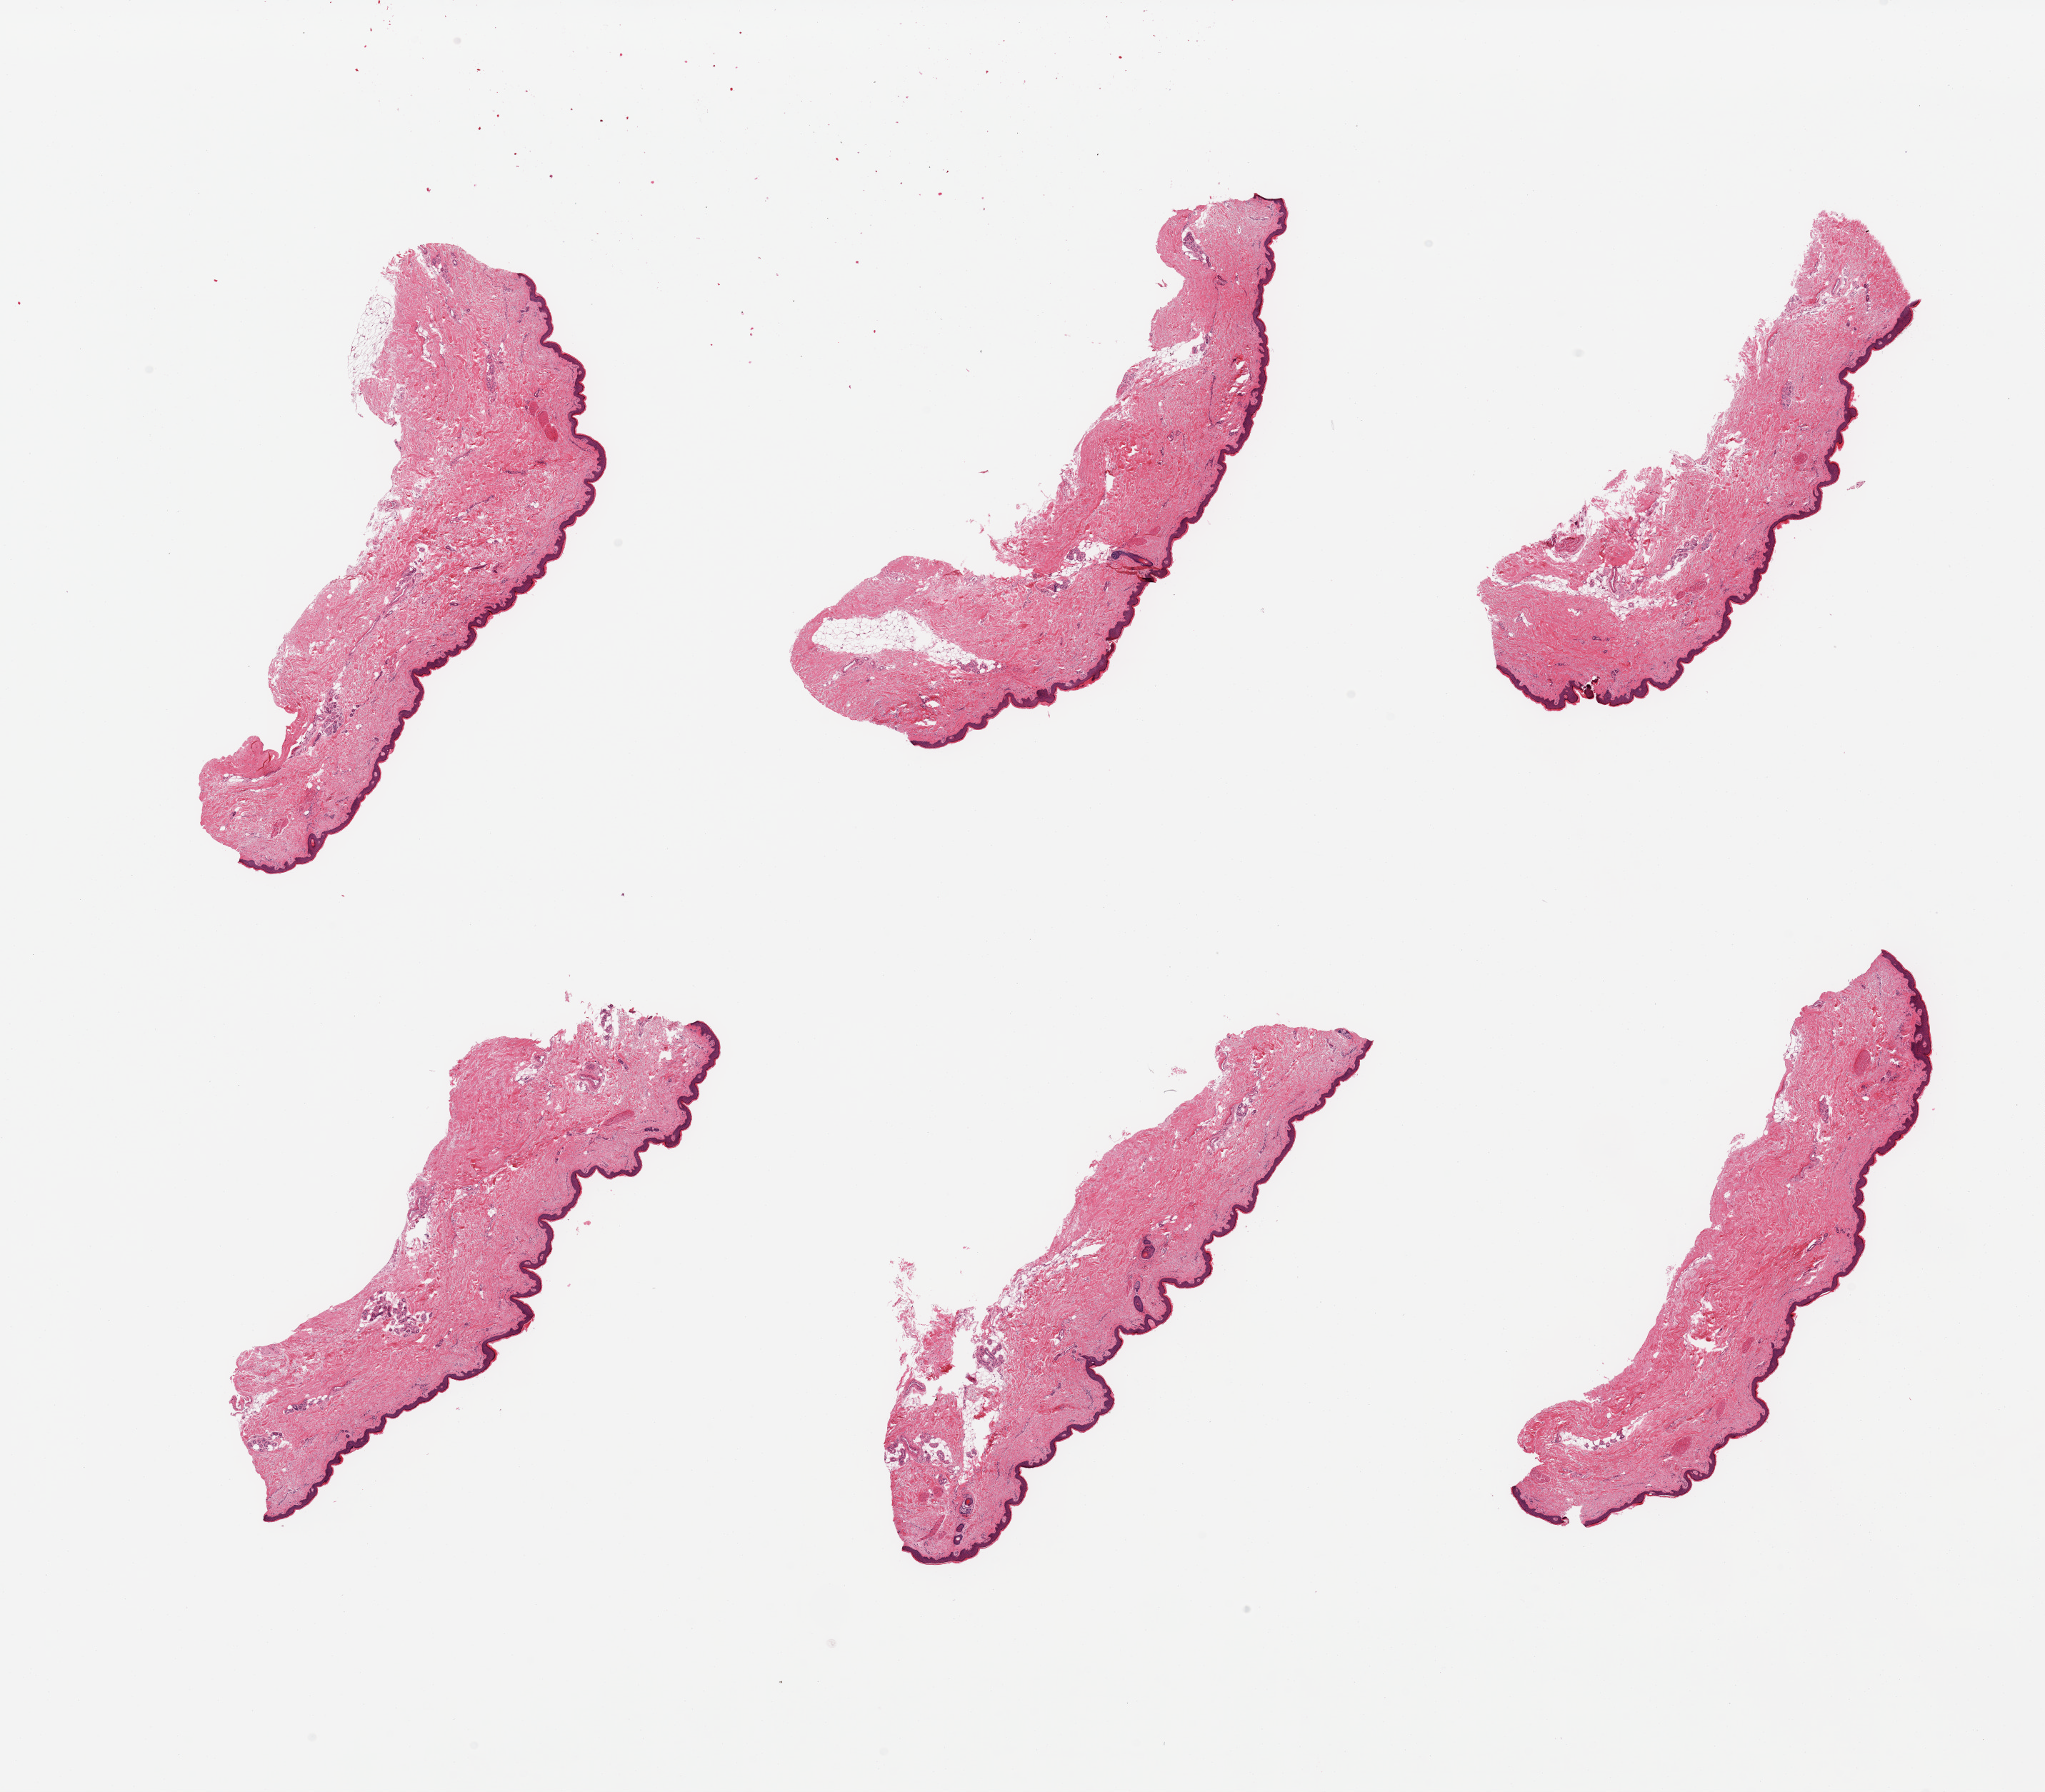
Digitized hematoxylin and eosin (H&E)-stained section, brightfield — a low-resolution overview of the entire scanned area, about 22.6 x 19.8 mm; PAXgene-fixed paraffin-embedded (PFPE) section; target tissue: skin of lower leg; tissue donor sample. Donor sex: female.
• review note (as recorded): 6 pieces, no dermal fat; squamous epithelium is ~40 microns